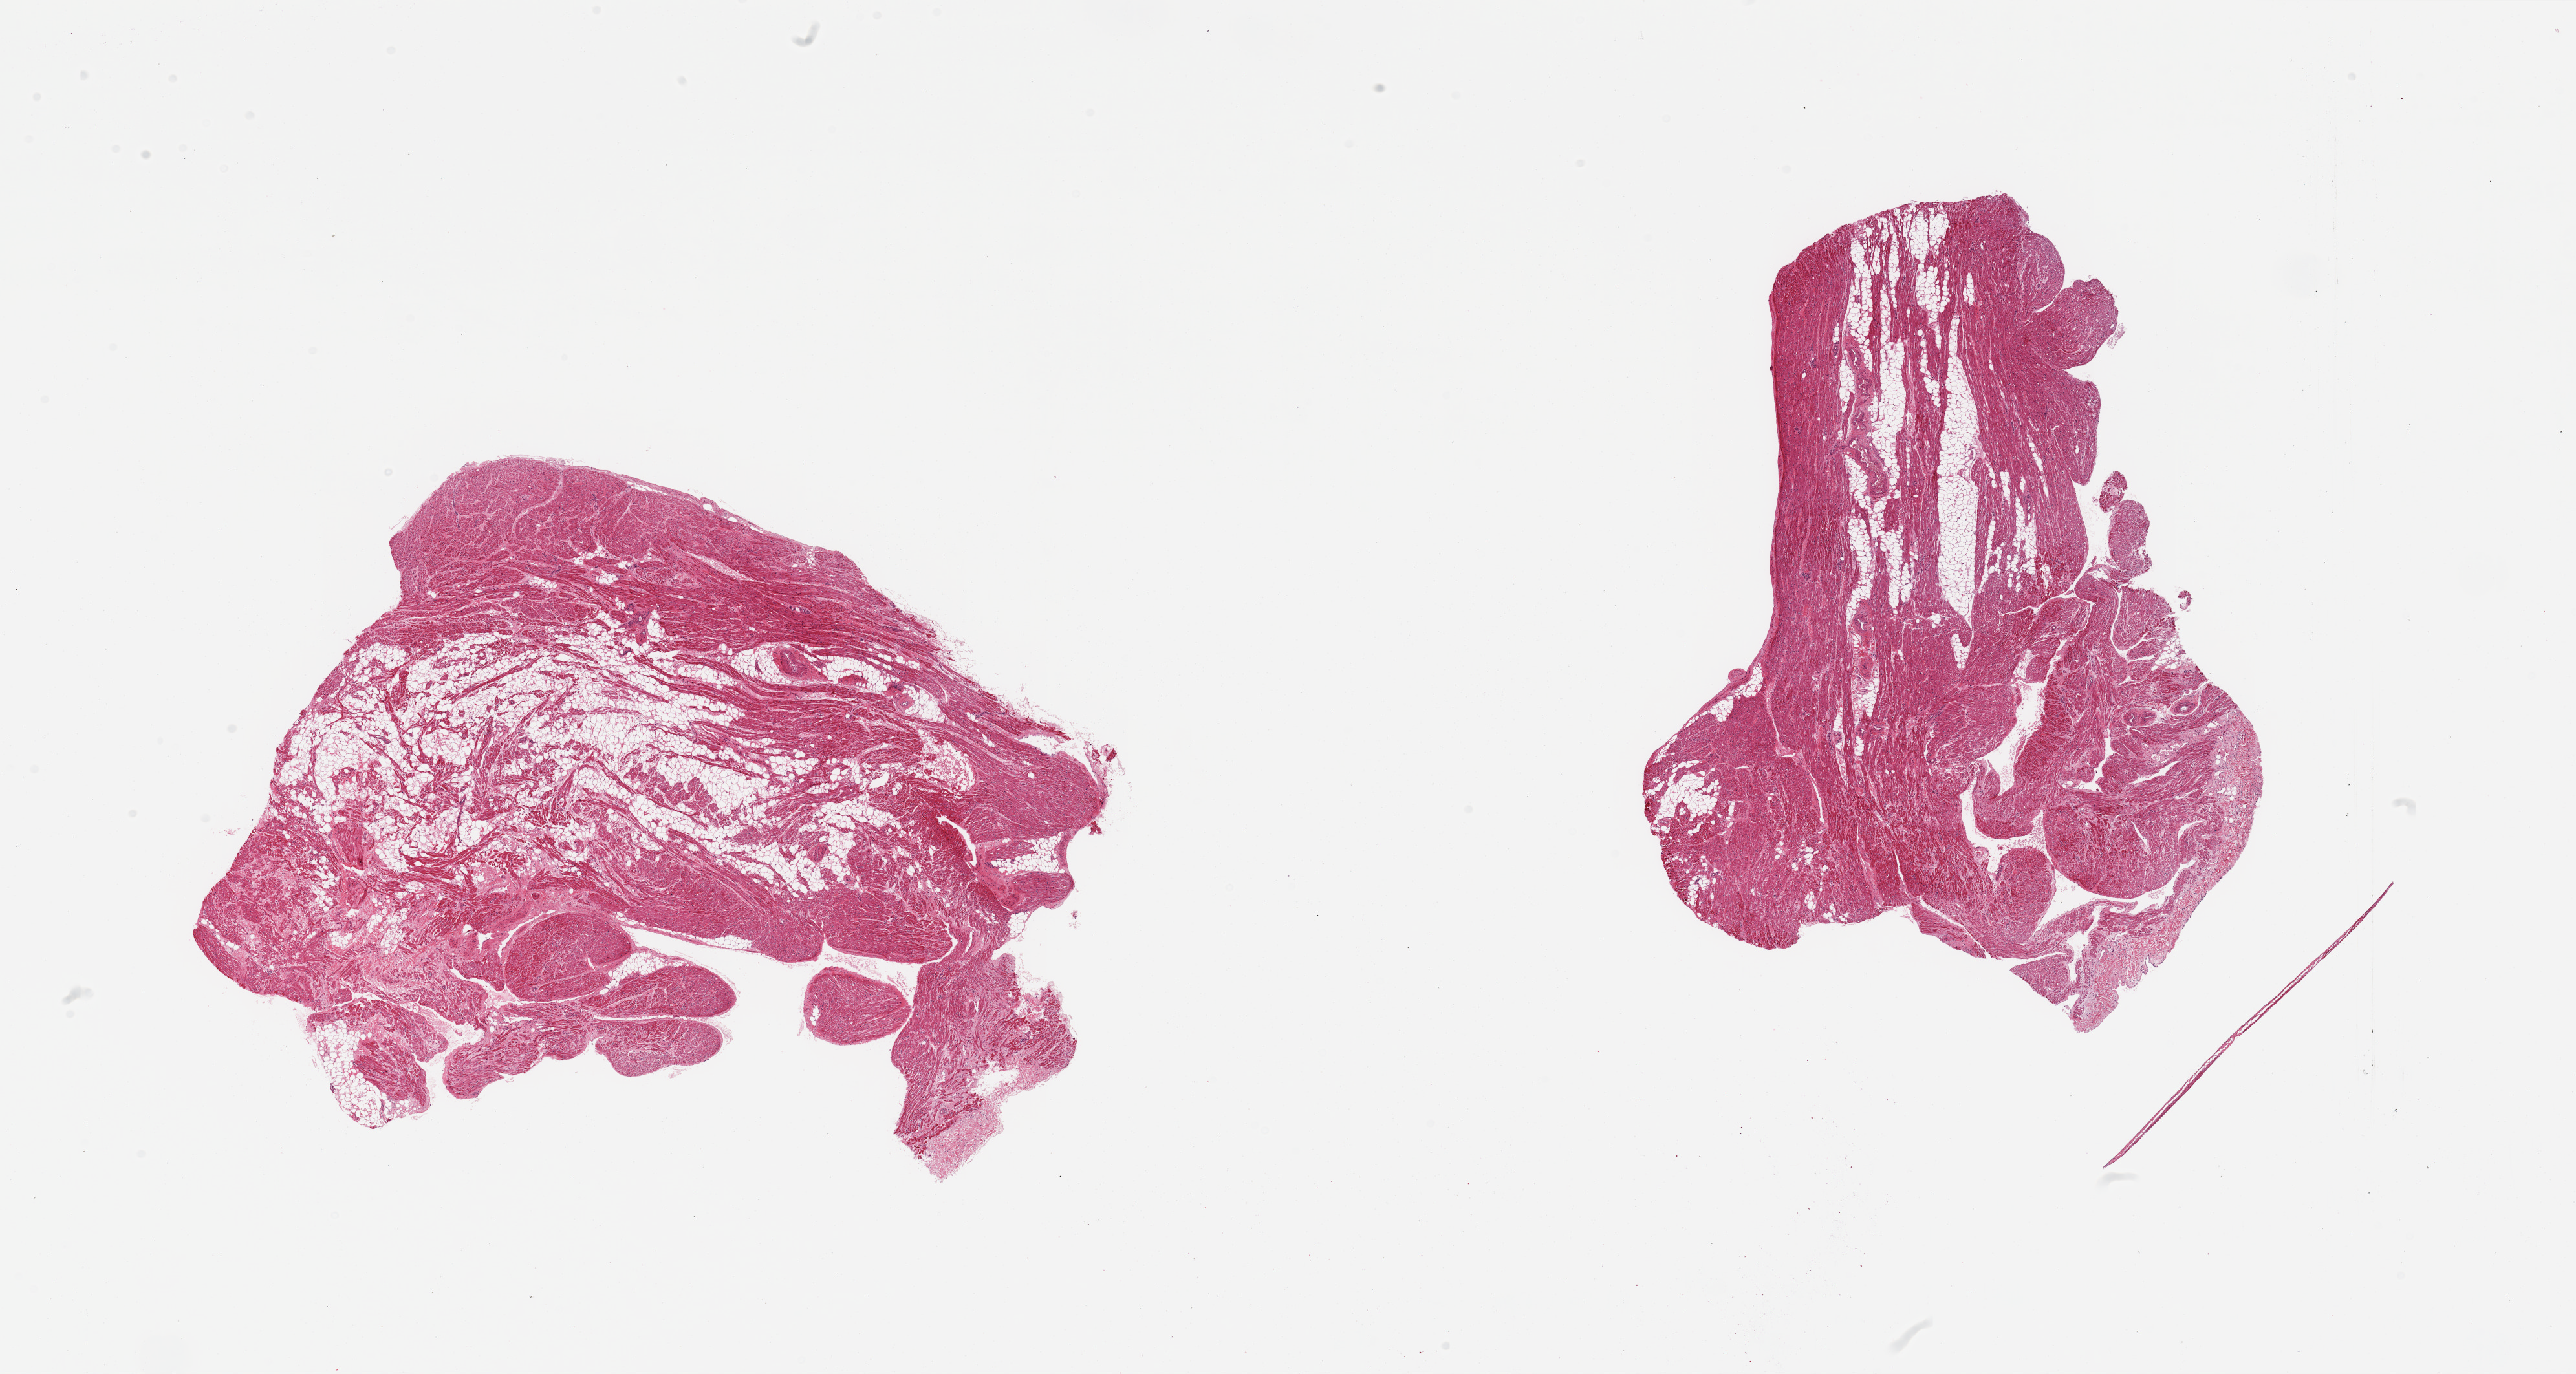
Whole-slide image, hematoxylin and eosin (H&E) stain — low-resolution overview of the scanned area, about 31.5 x 16.8 mm; PAXgene-fixed, paraffin-embedded tissue; target tissue: auricular appendage; tissue donor sample. Male donor.
• review note (as recorded): 2 pieces; 50% & 20% internal fat